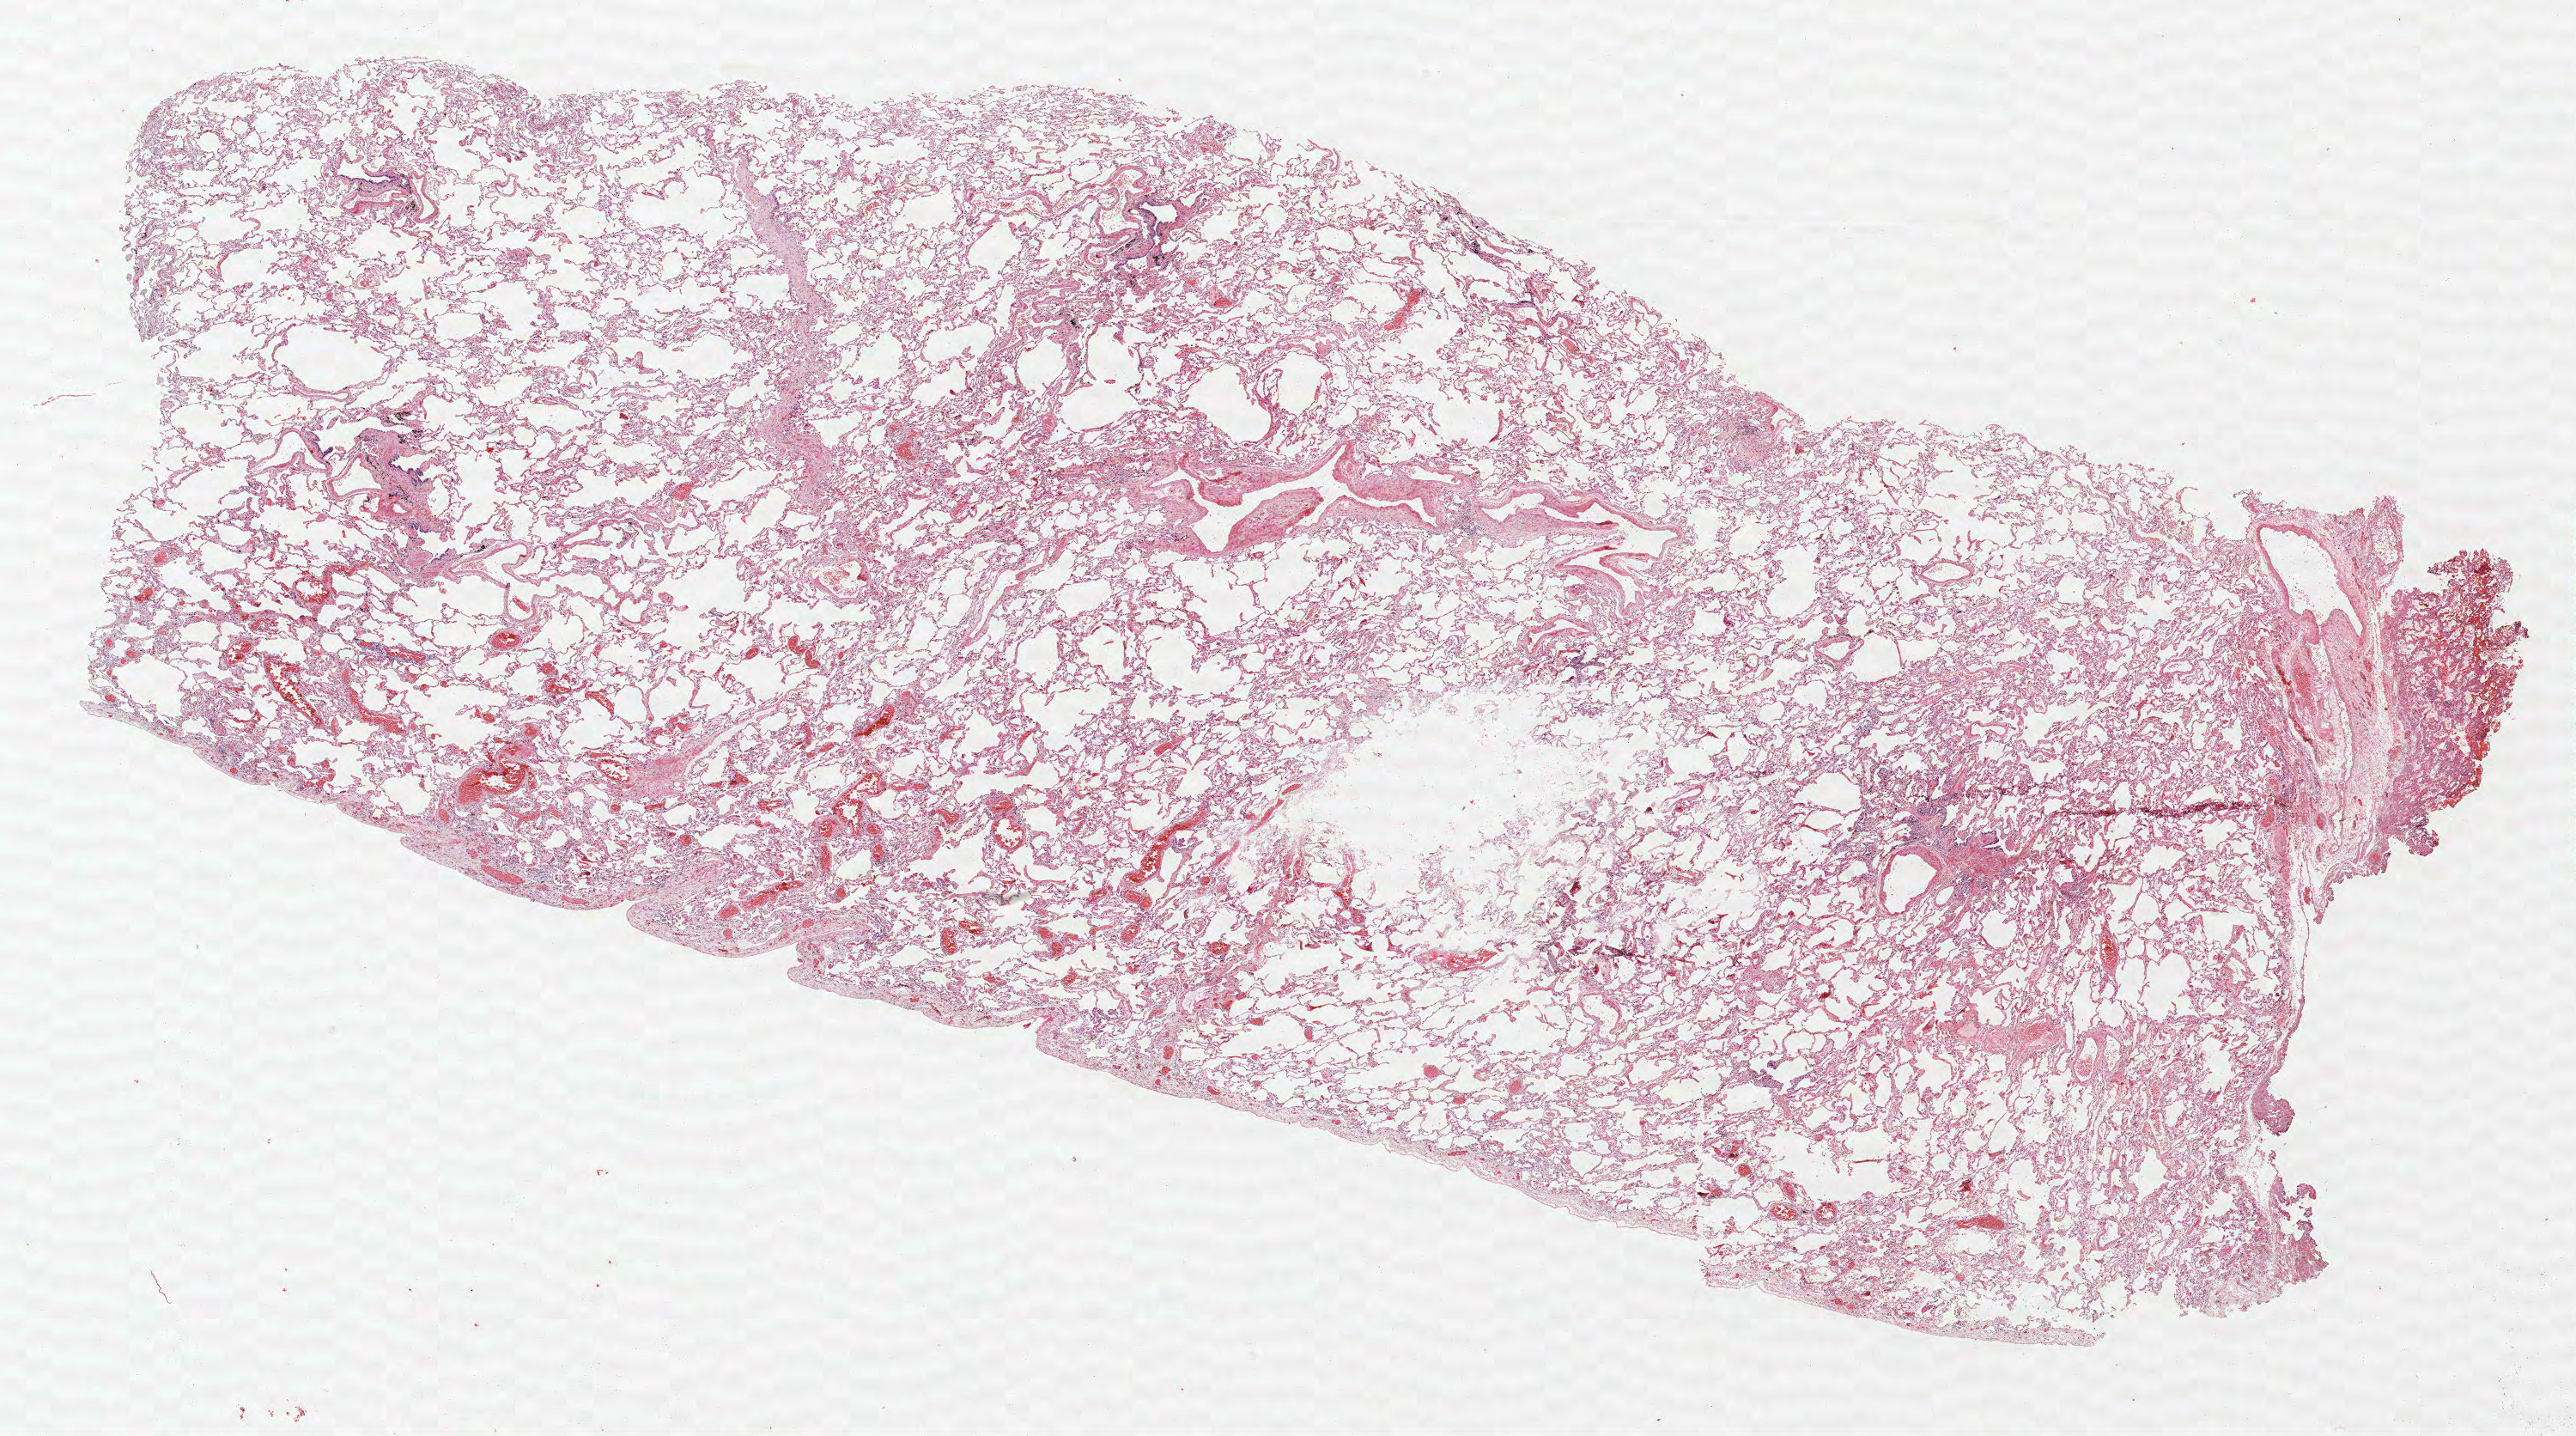
Whole-slide histology image, Hematoxylin and eosin (H&E) stained — whole scanned area (about 24.0 x 13.4 mm, slide scanned at 40x) shown as a low-resolution overview, formalin-fixed paraffin-embedded (FFPE) section, lung. Female, age 55 at enrolment. Former smoker at enrolment. Grade: well differentiated (G1).
• participant's lung-cancer diagnosis: Bronchiolo-alveolar adenocarcinoma, NOS
• stage (AJCC 6th edition): IA
• tumour size (pathology): 12 mm
• primary tumour location (clinical record): right lower lobe